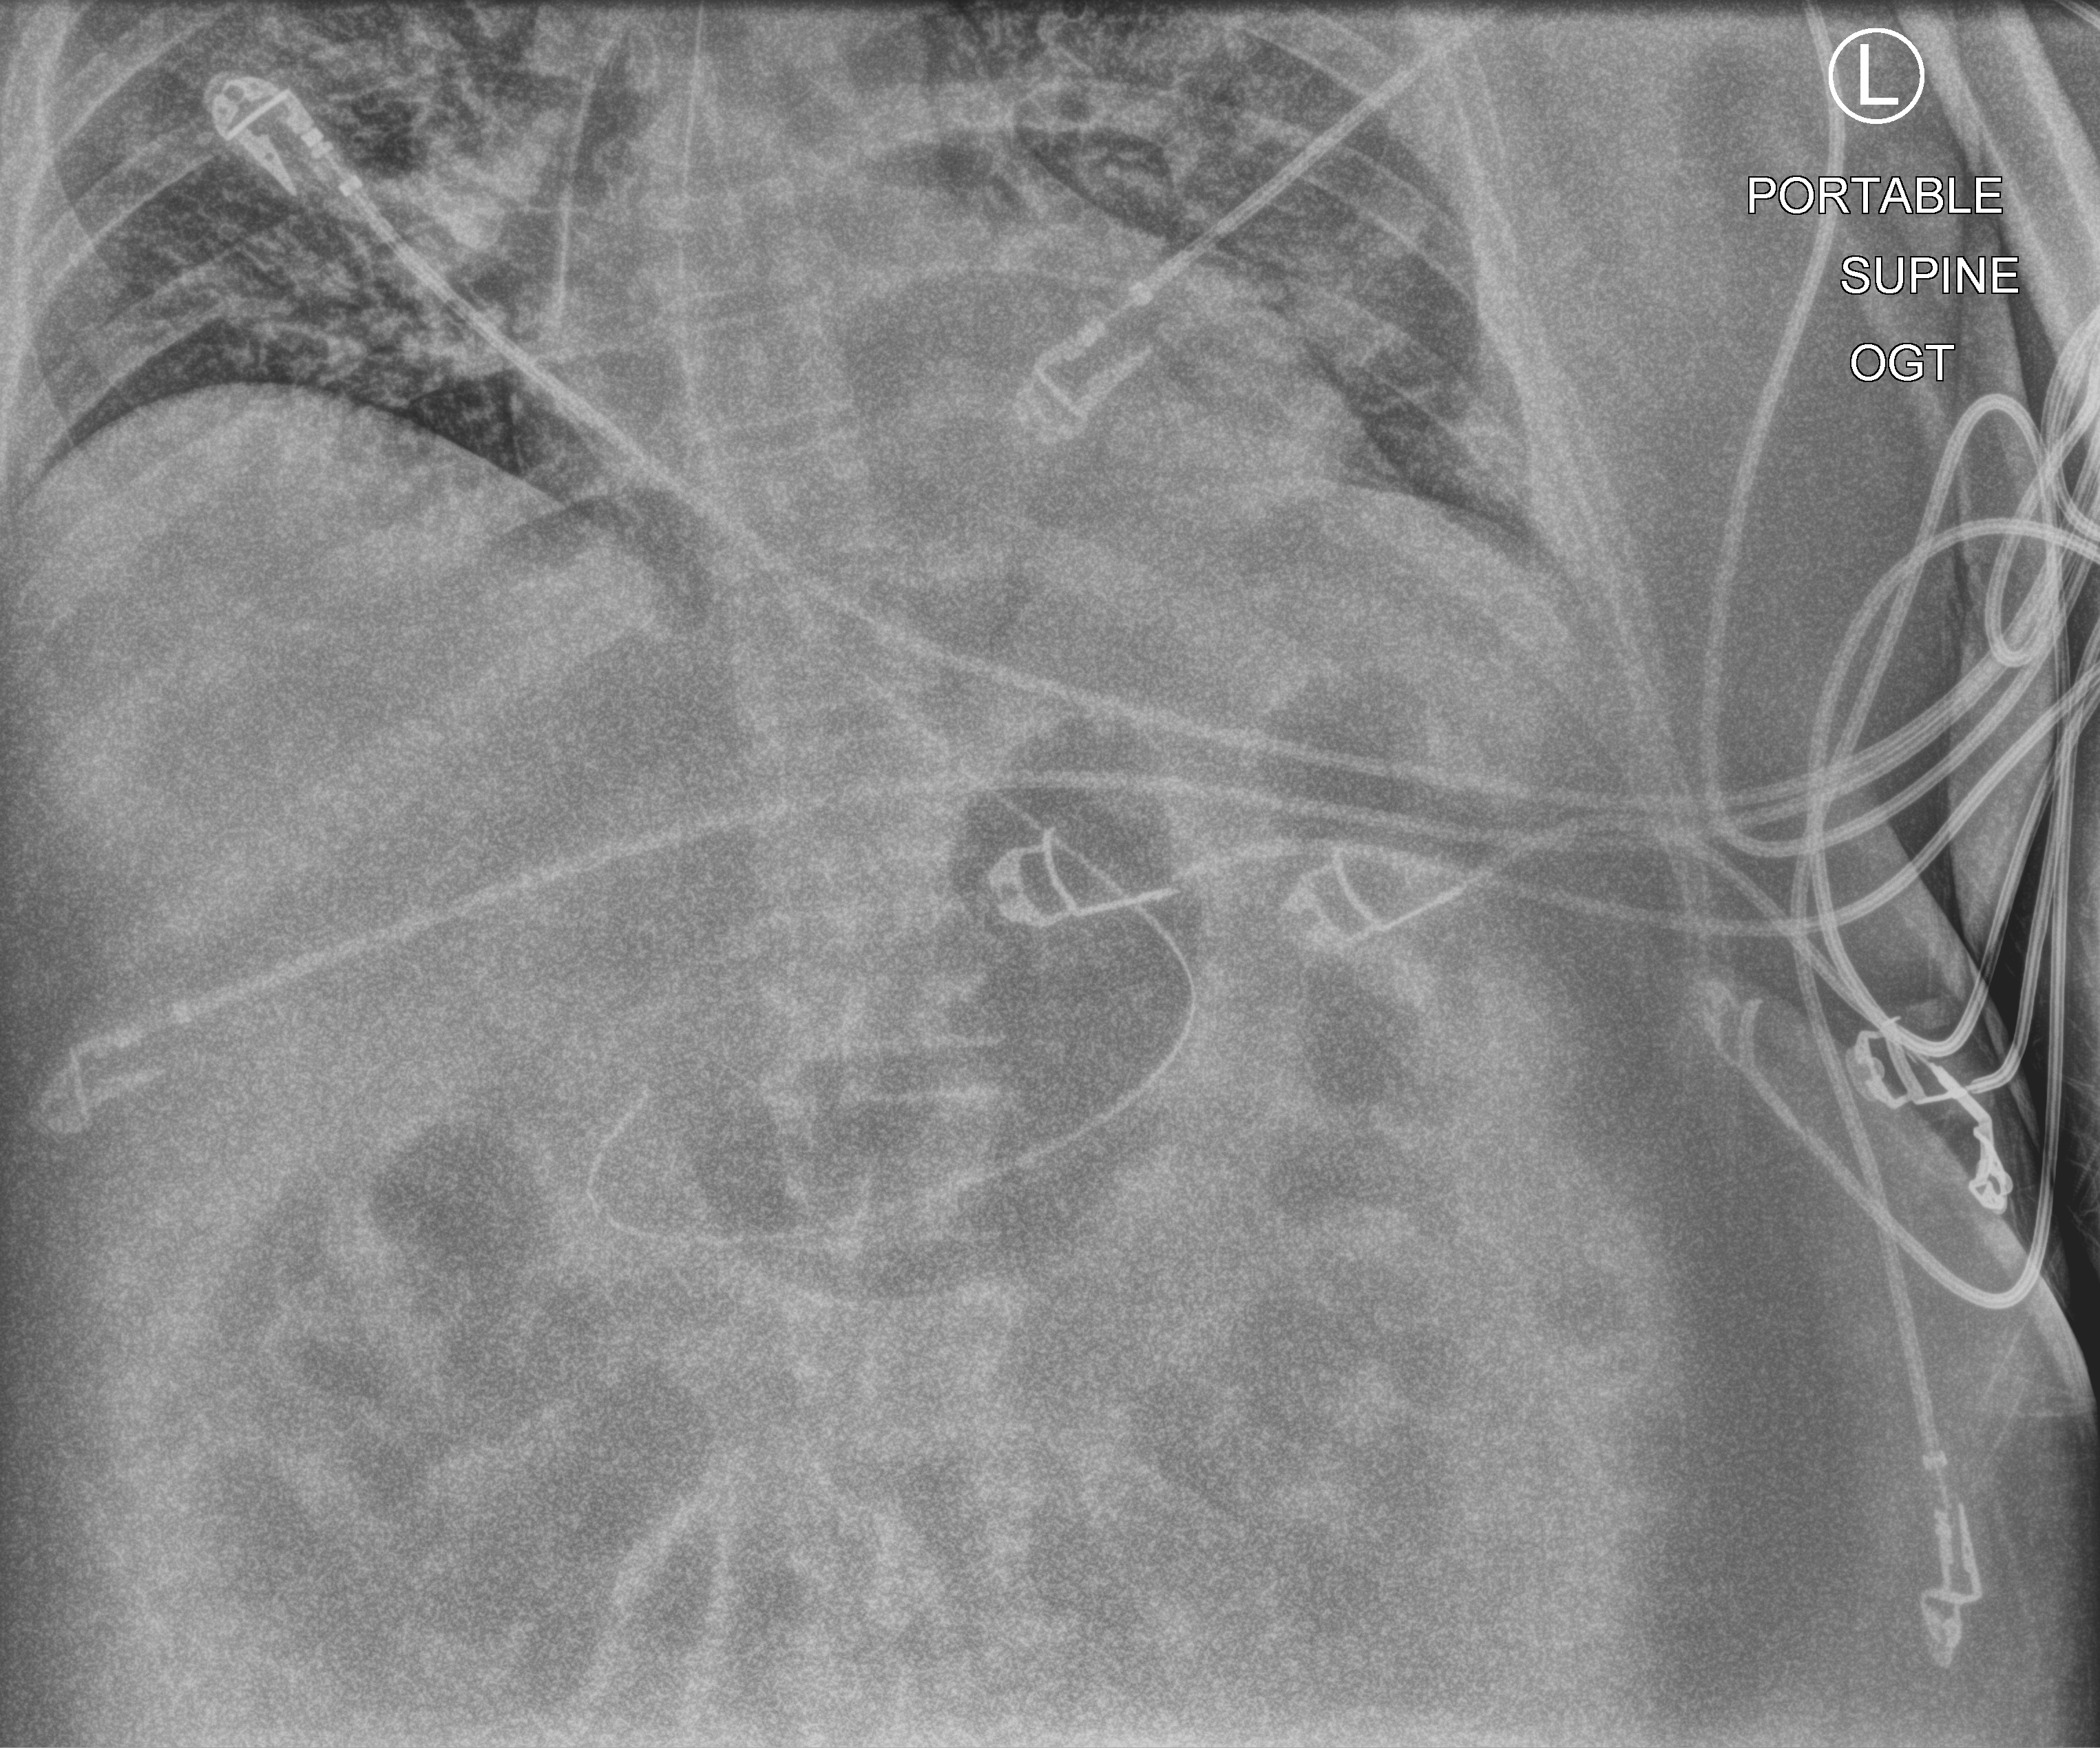
Portable abdomen radiograph; anteroposterior (AP) projection. Adult patient hospitalised with COVID-19, age 18–59 years.
Hospital-stay facts (about this admission, not read from this image; timing relative to this image not recorded): mechanically ventilated during this hospital stay: yes.